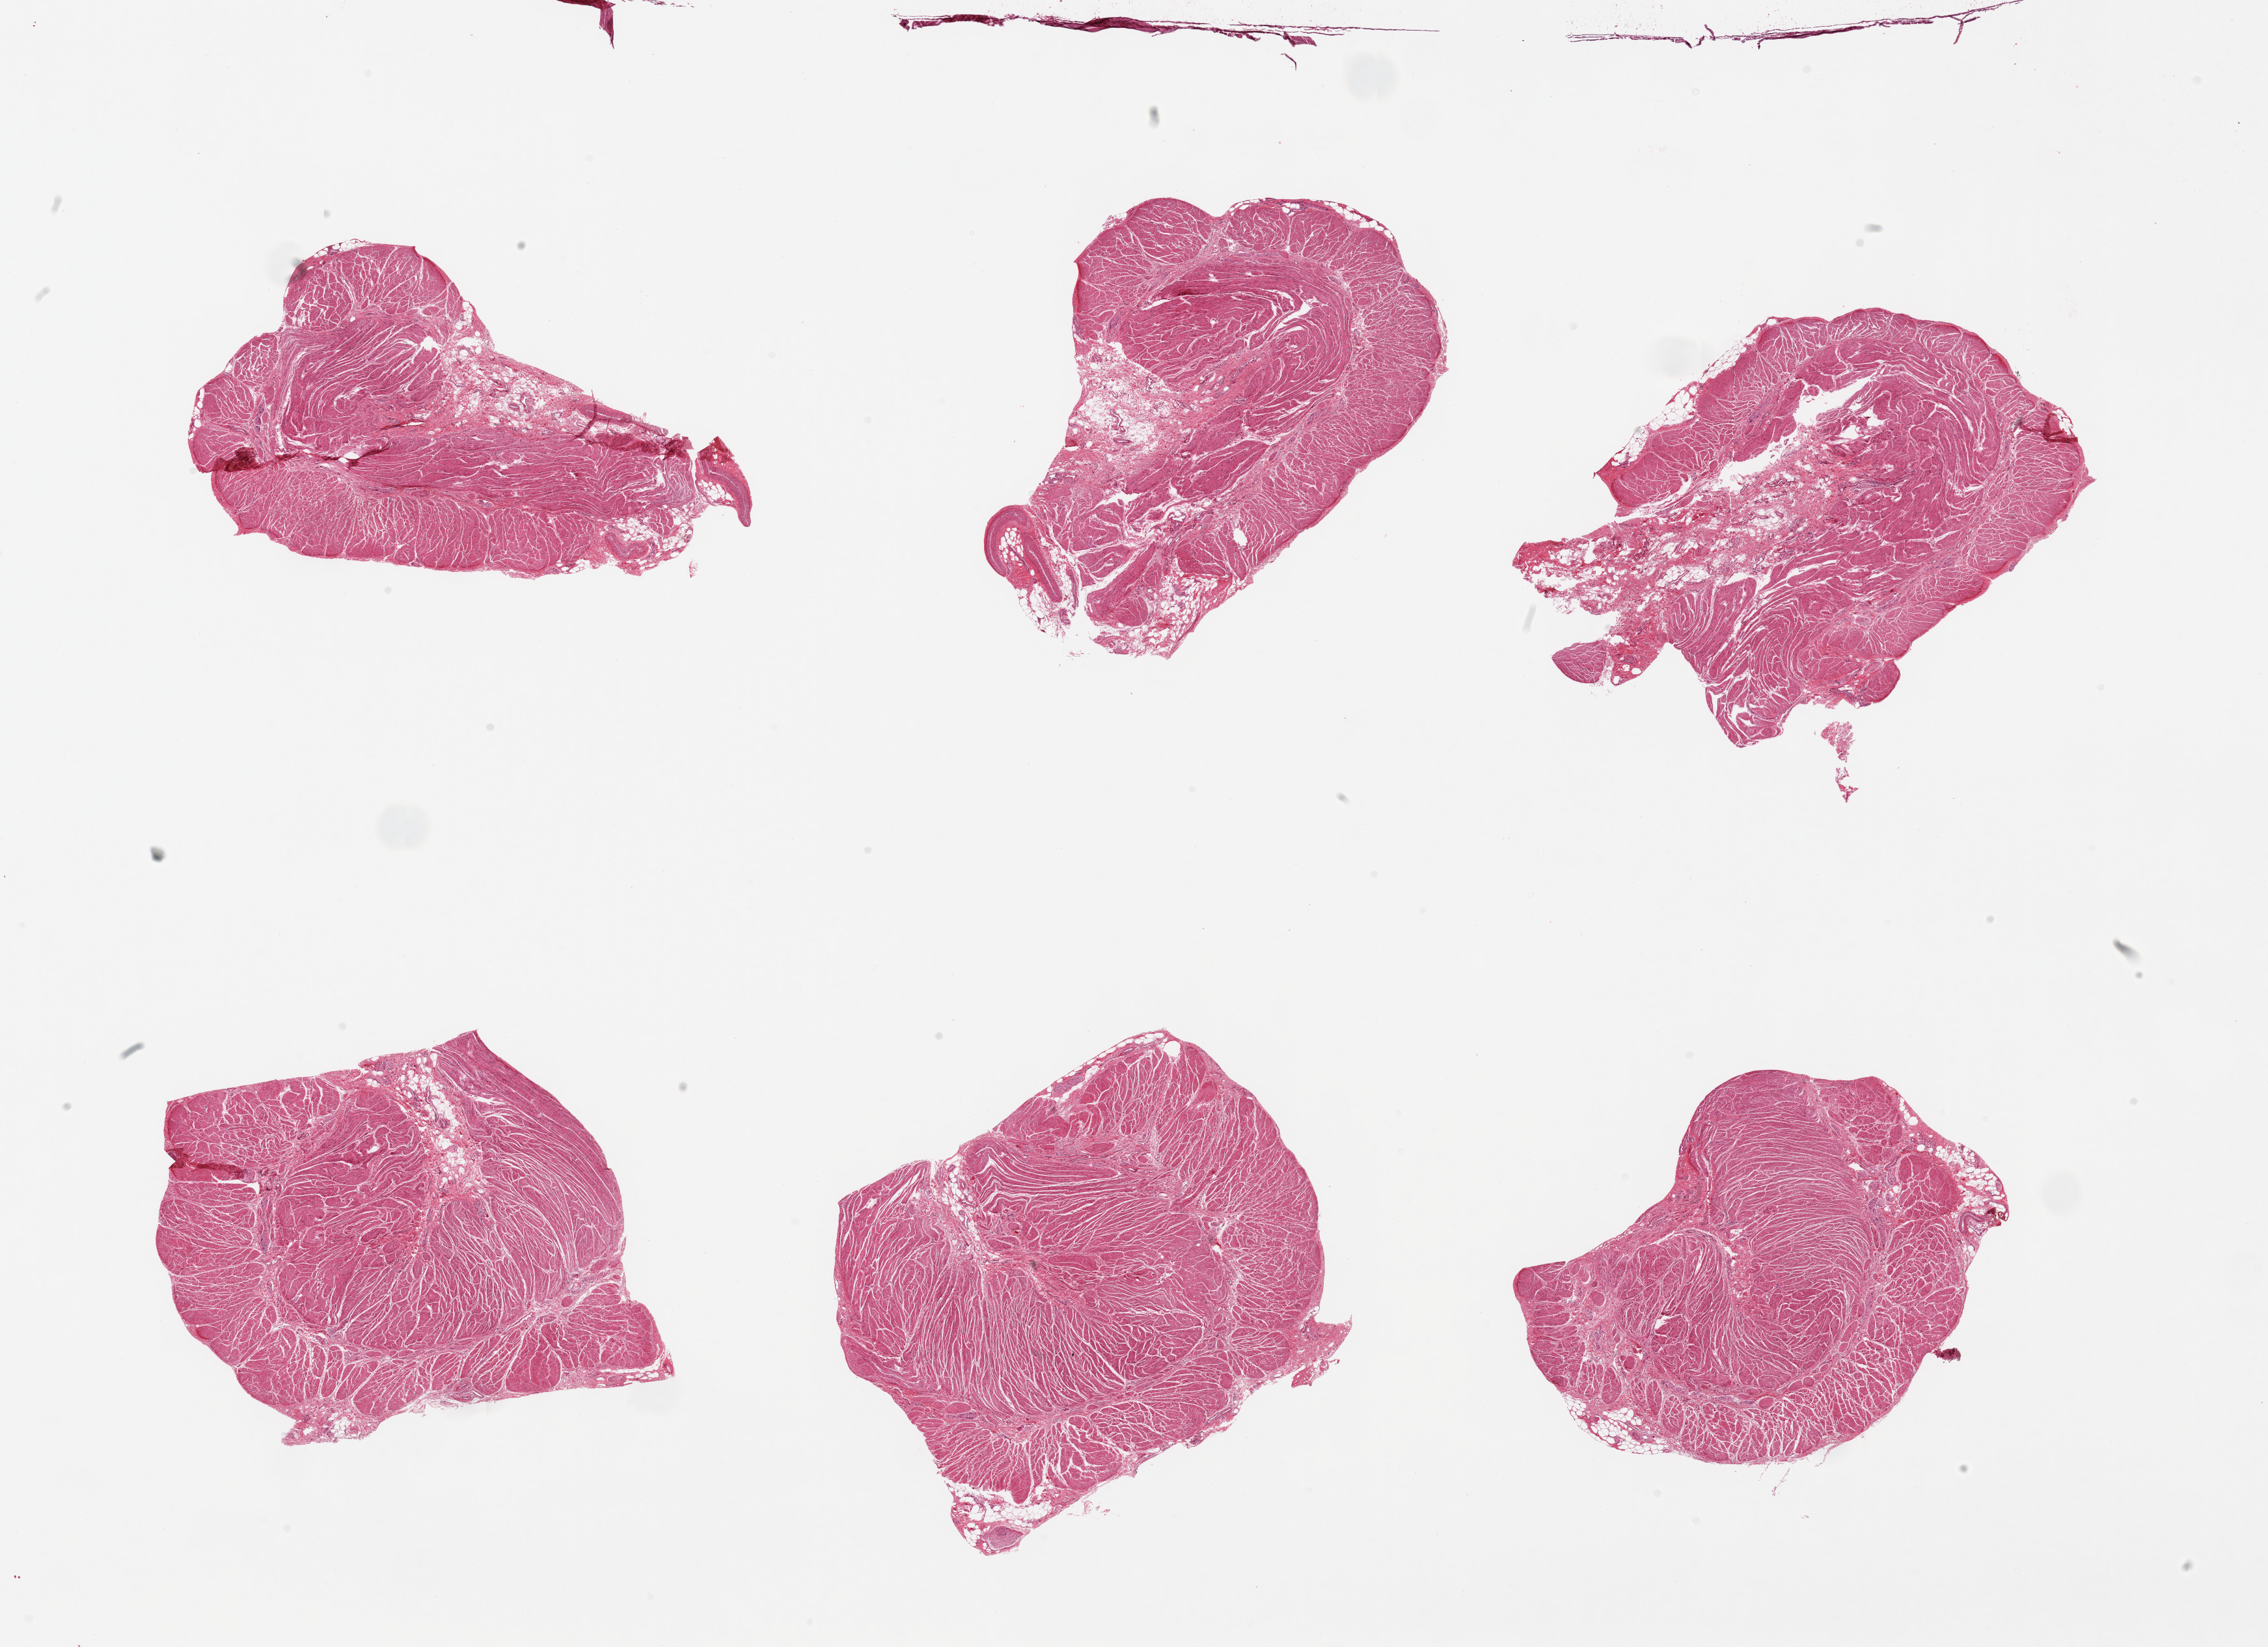
Haematoxylin and eosin whole-slide image, whole scanned area (about 27.6 x 20.0 mm, acquisition: 20x scan) shown as a low-resolution overview; PAXgene-fixed, paraffin-embedded tissue; section of gastroesophageal junction (target tissue); tissue donor sample. Donor sex: male.
Pathologist's review note for this sample: 6 pieces; free of mucosa, some larger vessels present.